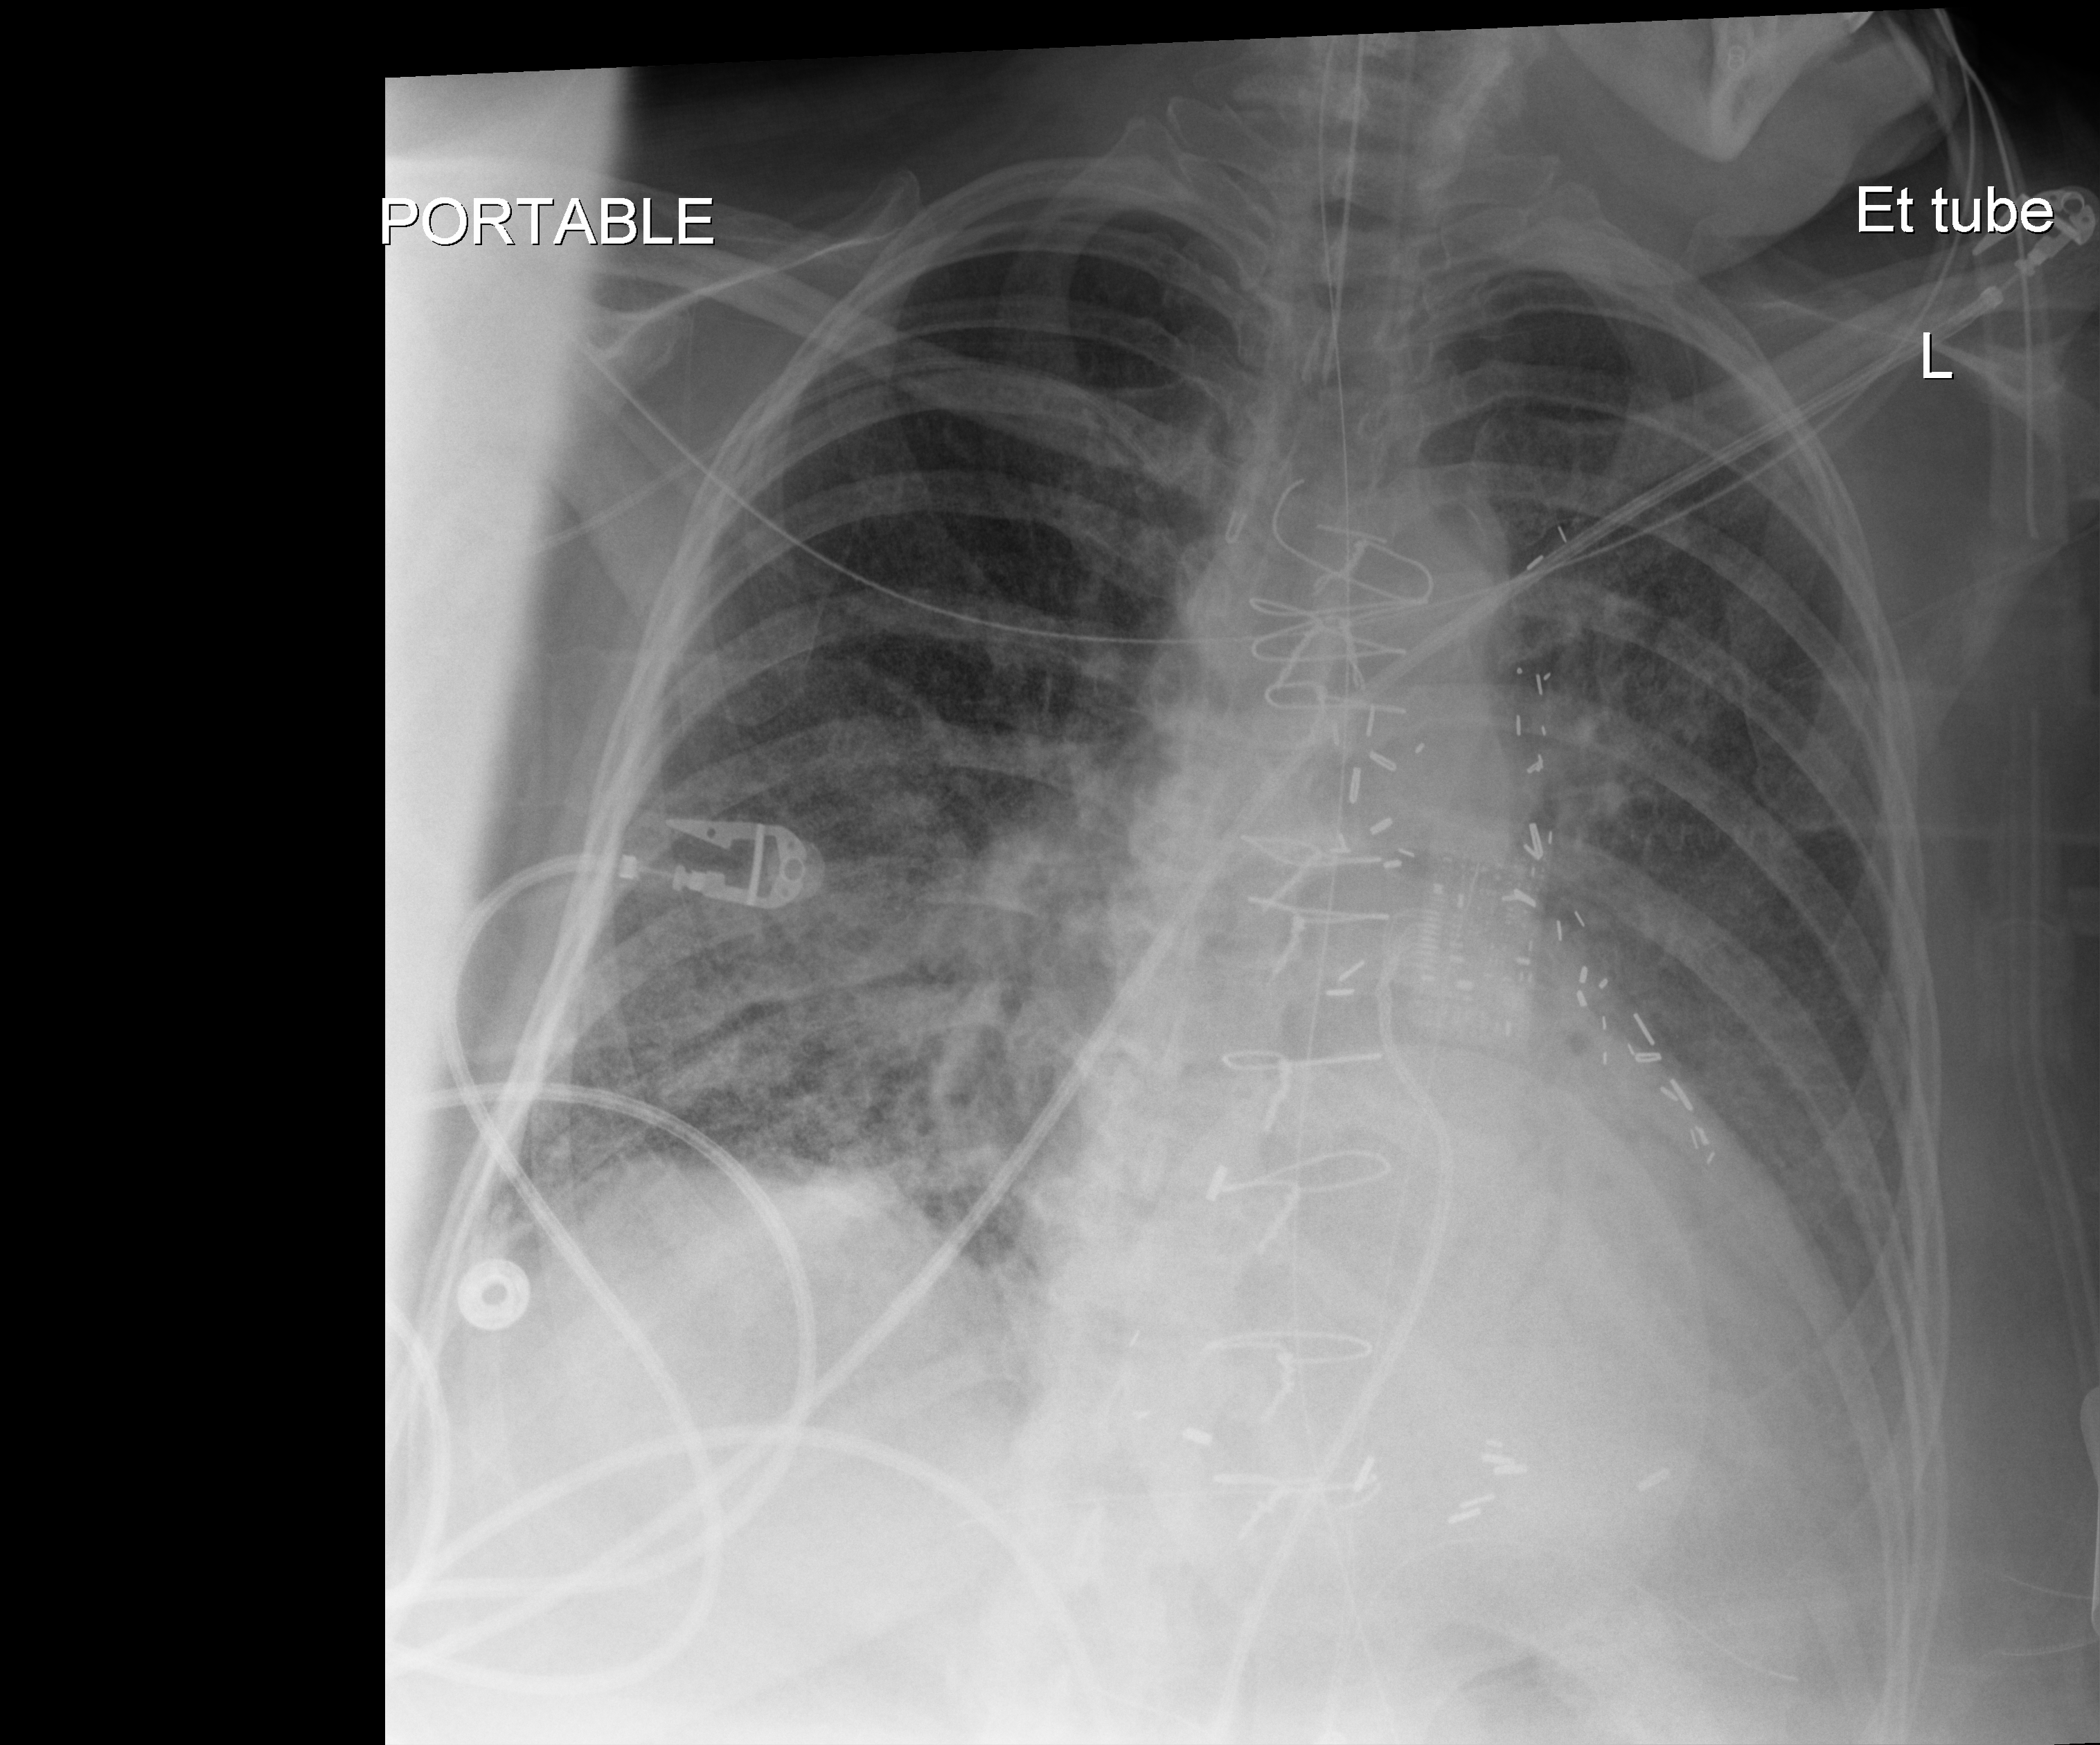
Portable chest radiograph; anteroposterior (AP) projection. Female patient hospitalised with COVID-19, age 60–74 years.
From the hospital-stay record, not from the radiograph (when in the stay this image was taken is not recorded): length of hospital stay: 25 days; smoking status (admission record): never.